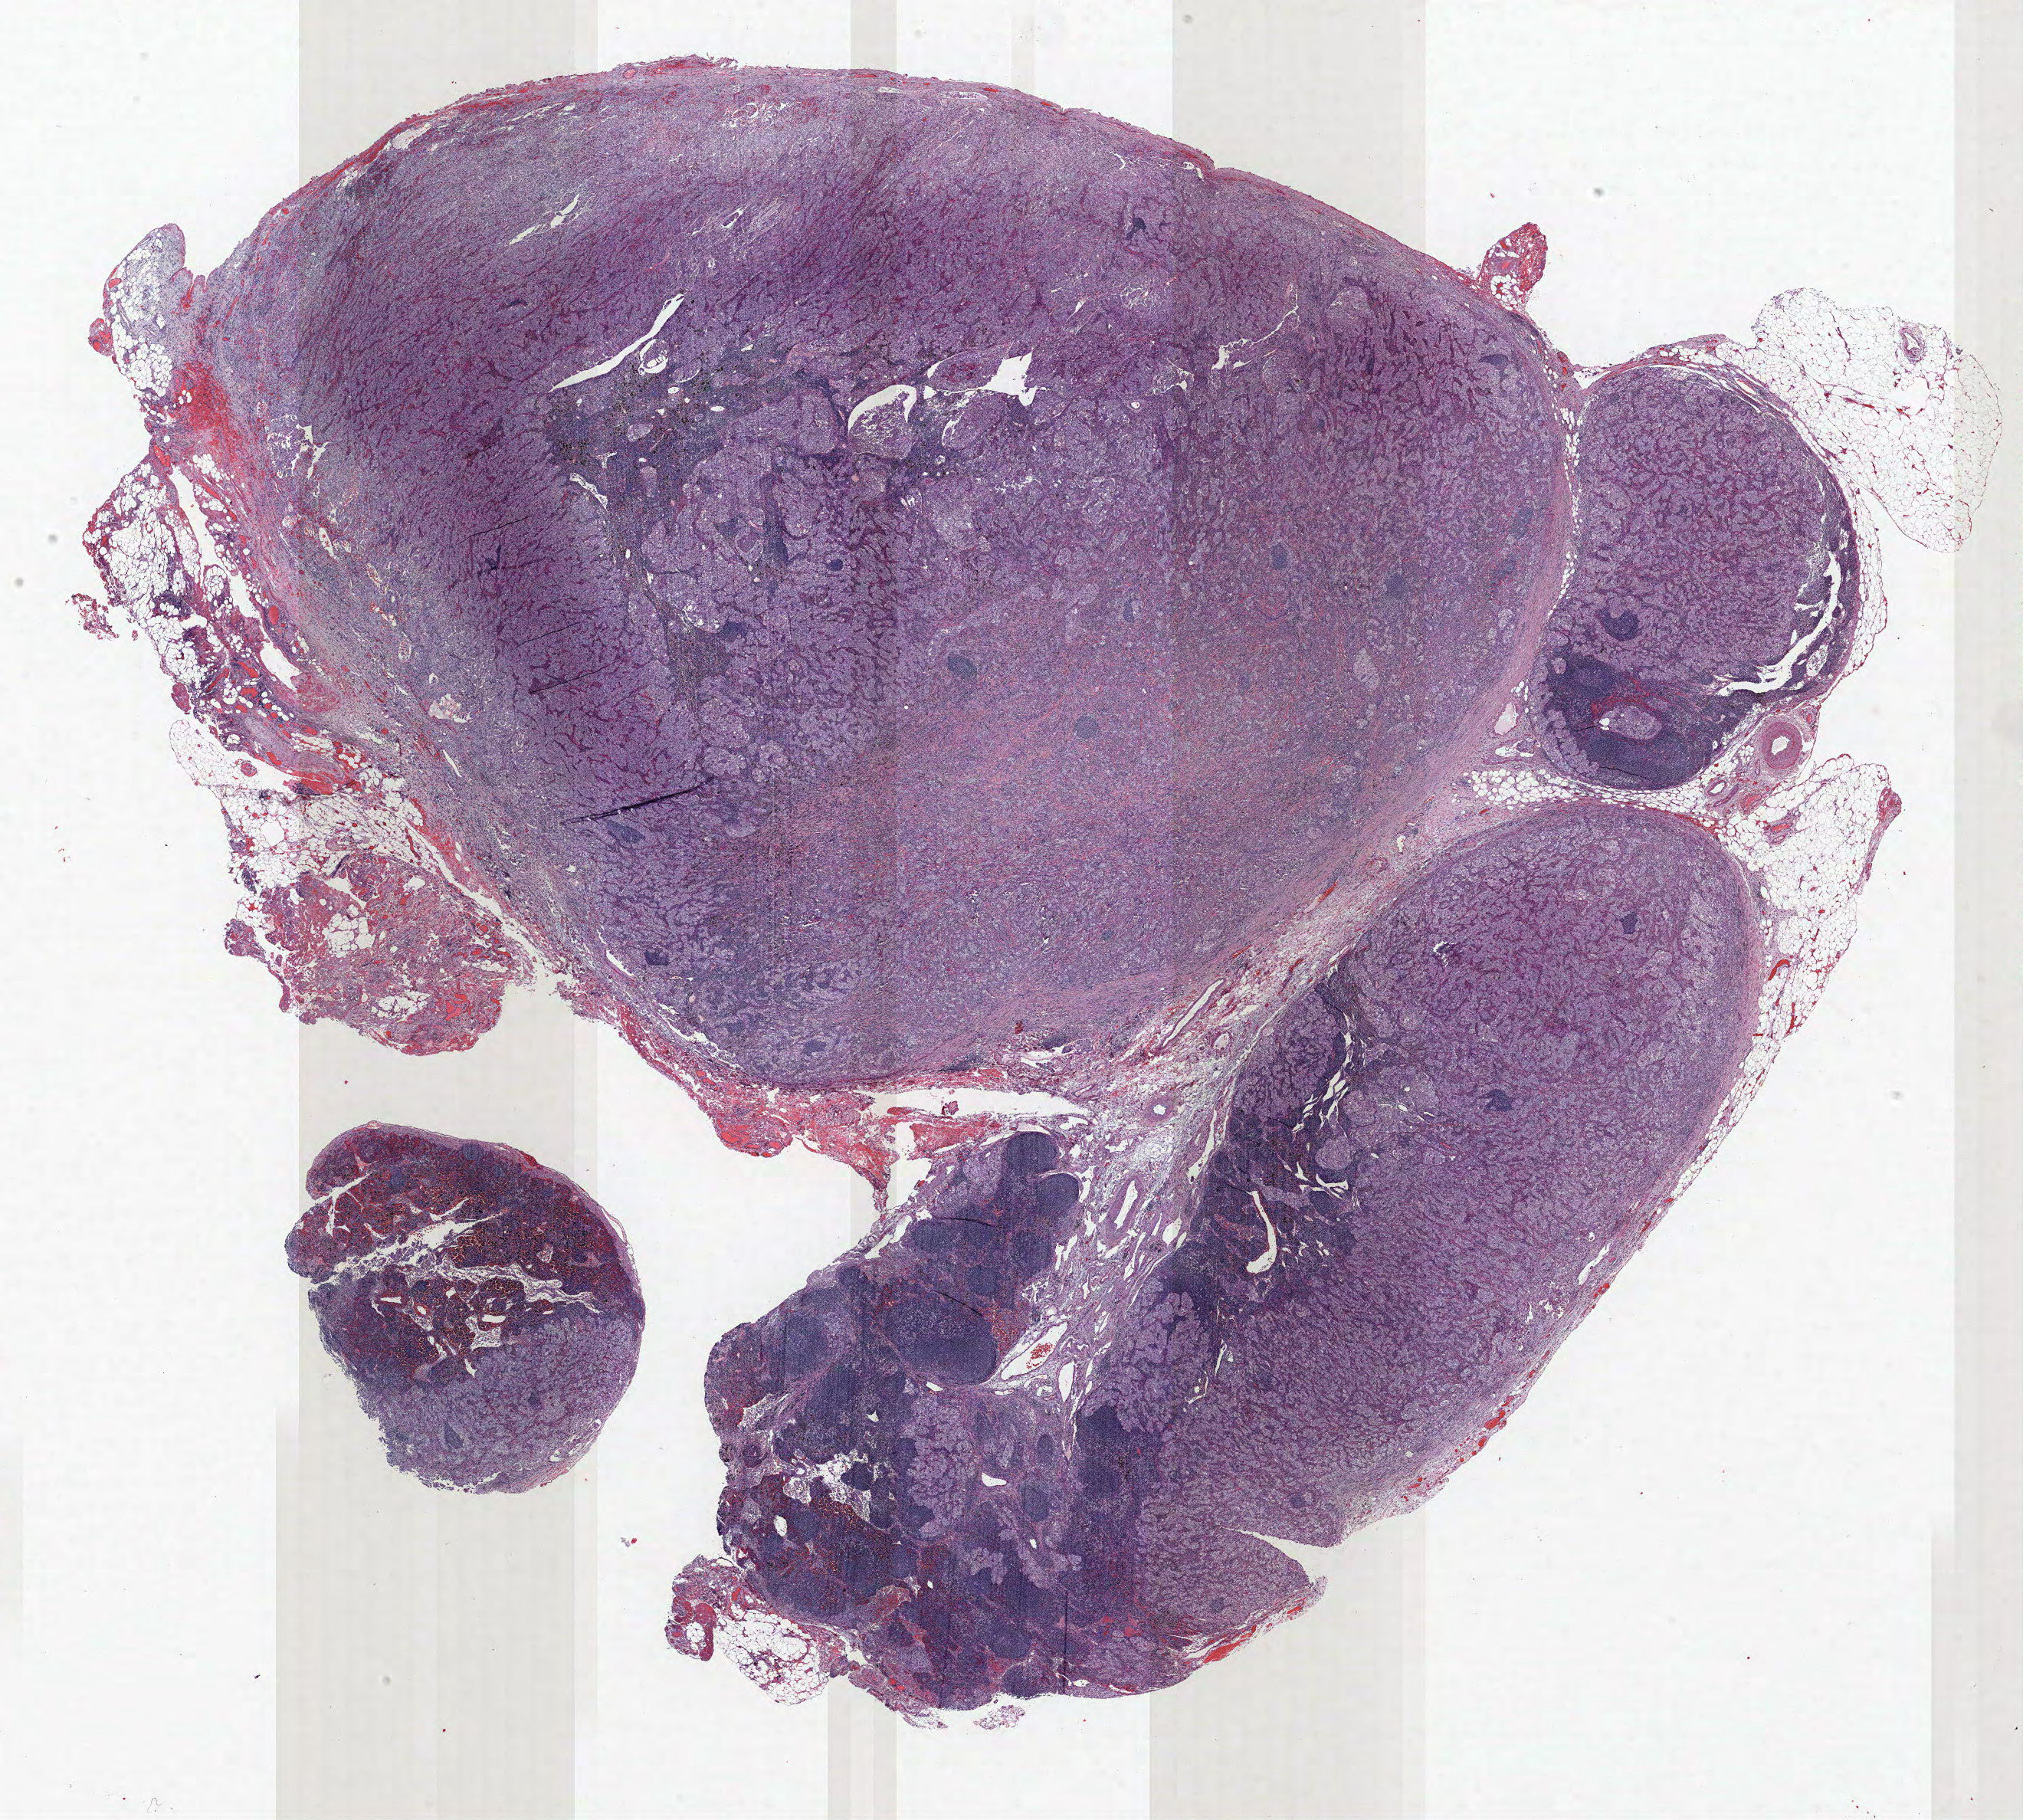
Hematoxylin and eosin (H&E) stained whole-slide image — whole scanned area (about 21.1 x 19.0 mm, from a 40x scan) shown as a low-resolution overview, formalin-fixed paraffin-embedded (FFPE) section, lung tissue. Female, age 61 at enrolment. Former smoker at enrolment. Grade: poorly differentiated (G3).
• participant's lung-cancer diagnosis: Adenocarcinoma, NOS
• stage (AJCC 6th edition): IIIA
• tumour size (pathology): 22 mm
• primary tumour location (clinical record): right upper lobe